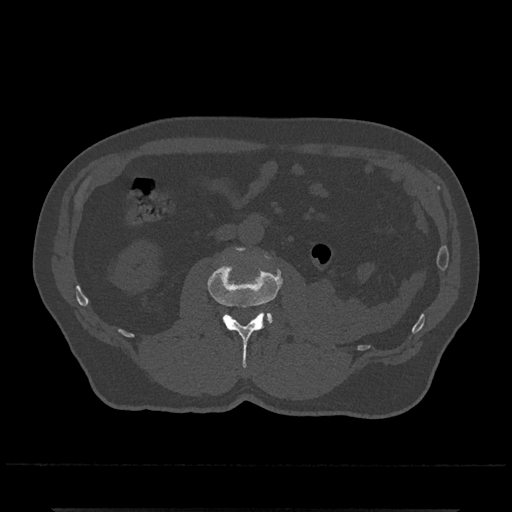
CT including the spine, one axial slice. Reconstruction kernel Br40s/3. 120 kVp. Bone window (W 1800 / L 400 HU). 0.5 mm slice thickness. 512 × 512 image matrix, field of view 393 × 393 mm. Male patient, age 67 years. Case-level facts recorded for this patient, not image findings: primary cancer: prostate.
Outlined on this slice (semi-automatically segmented with operator editing):
- L2 vertebra: bounding box <208,247,283,368> (left, top, right, bottom; pixels)
- L3 vertebra: <258,311,273,324>